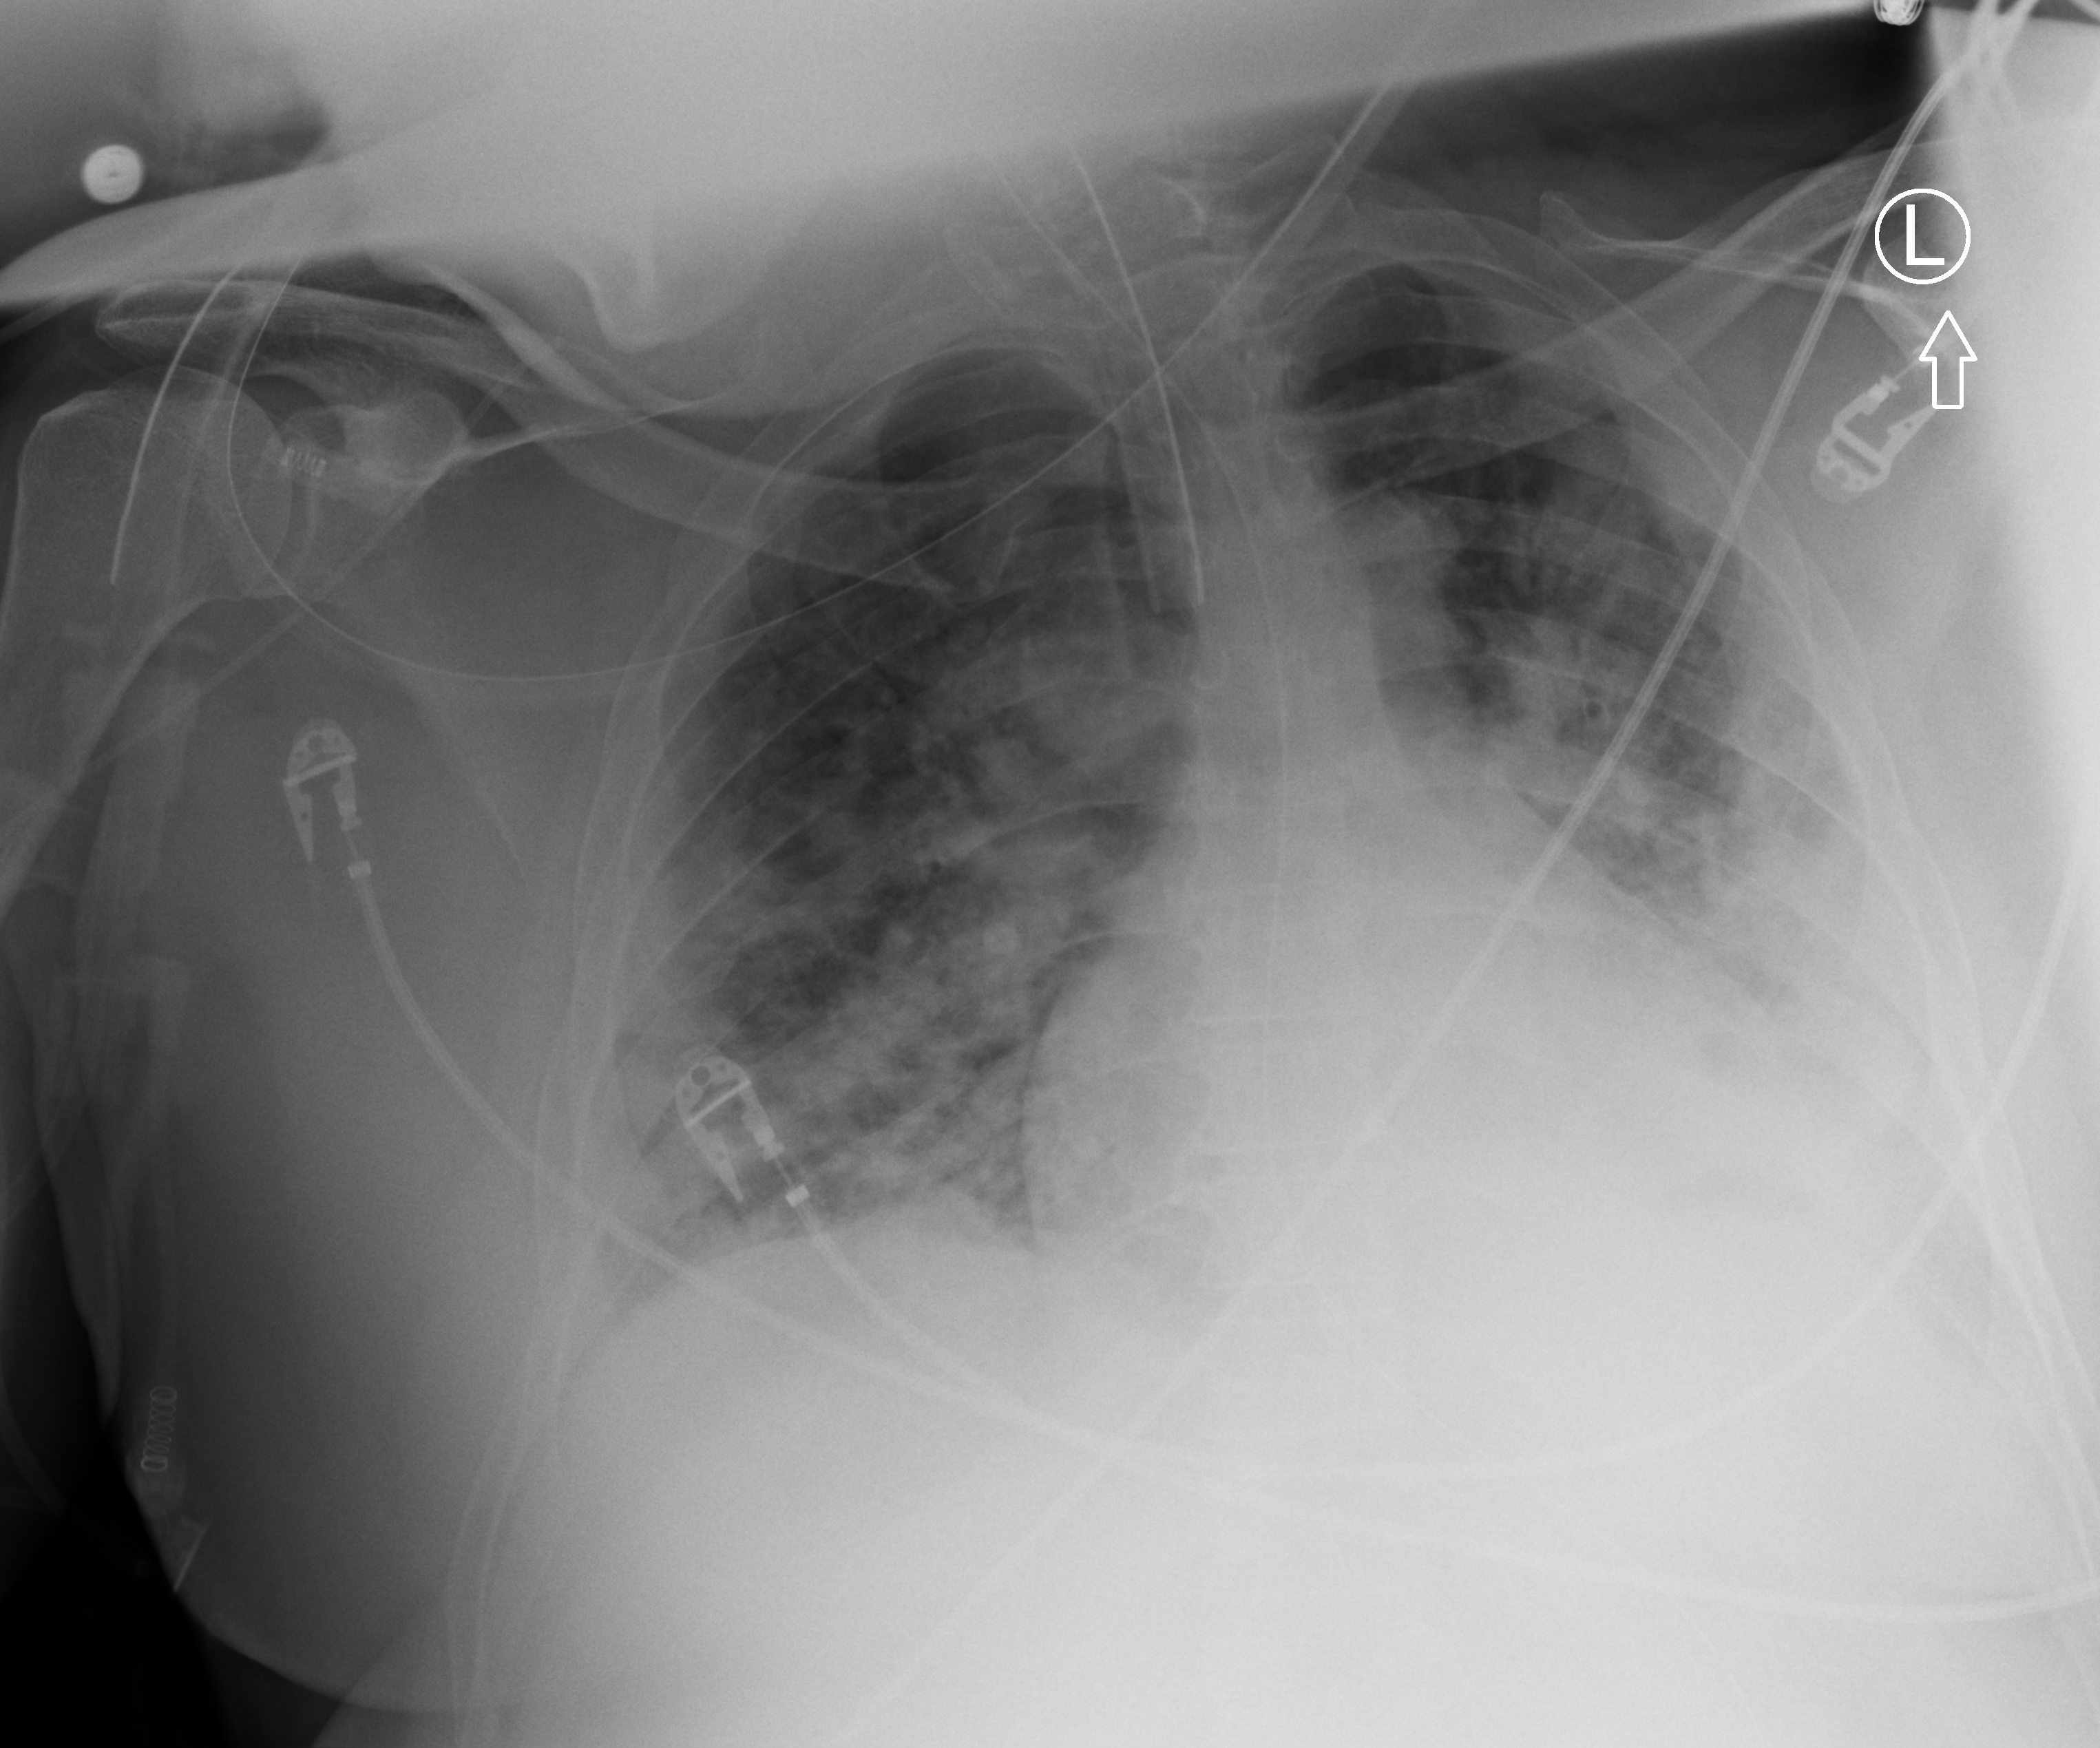
Portable chest radiograph. Patient hospitalised with COVID-19; male, aged 18–59 years.
Admission-level facts for this patient (not findings on this image; timing relative to this image not recorded):
- admitted to intensive care during this hospital stay: yes
- diabetes (admission record): no